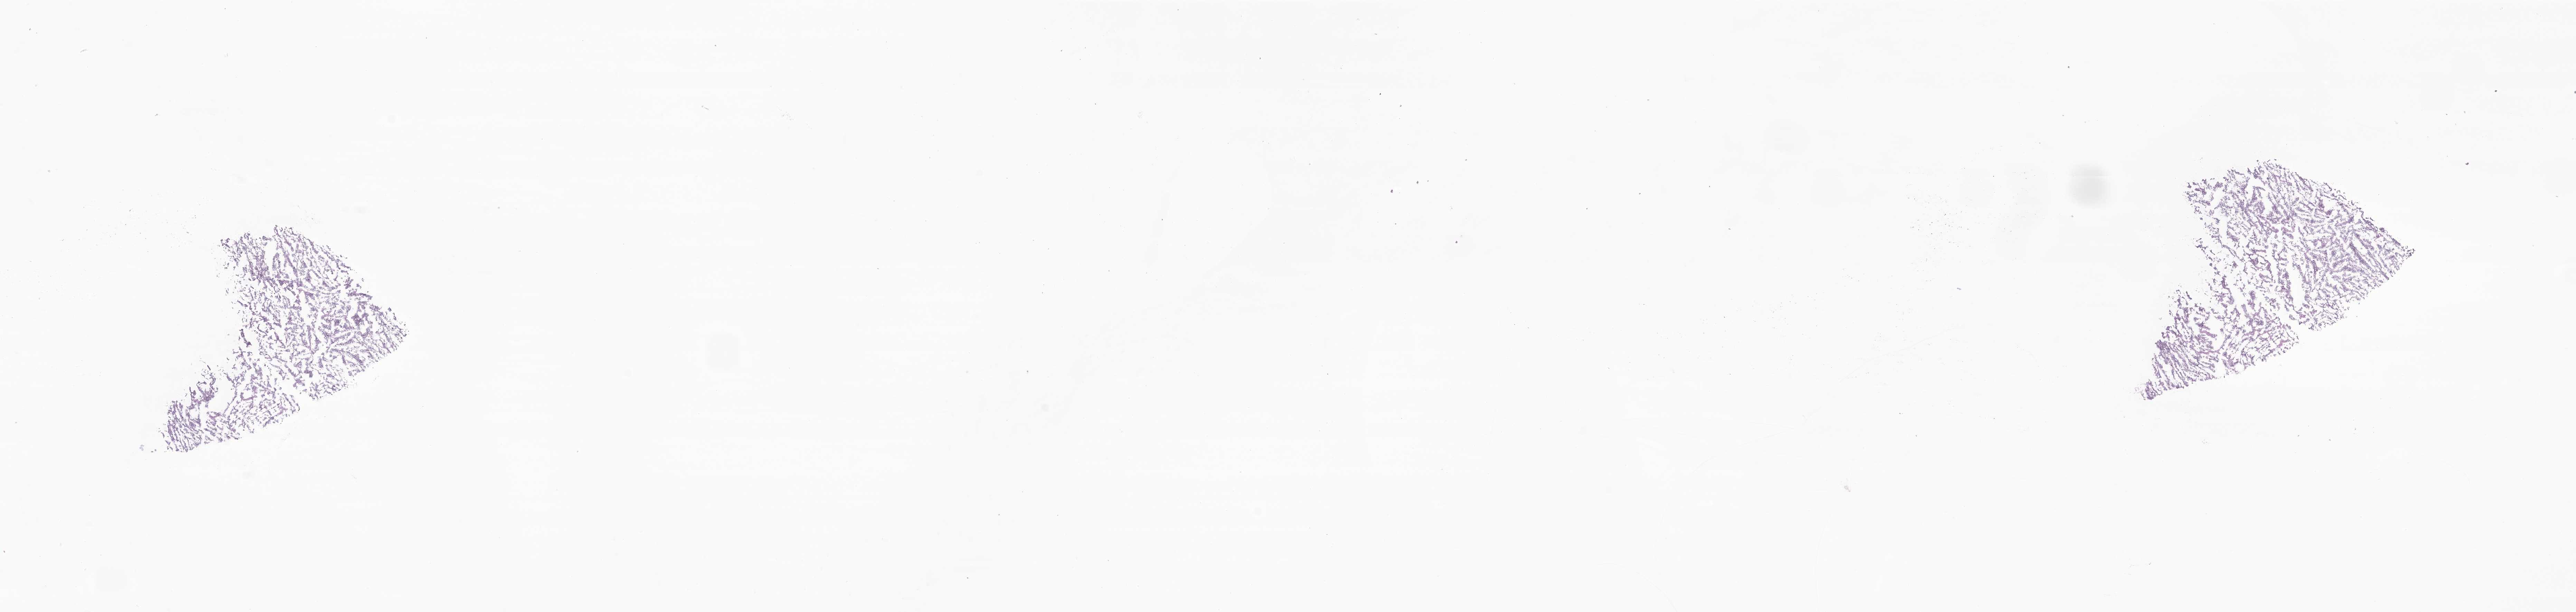
Haematoxylin and eosin whole-slide image of tumor tissue from the frontal lobe — shown as a low-resolution overview of the whole scanned area (about 31.4 x 7.5 mm). Frozen section (OCT-embedded). Patient: female, age 122 months (10 years 2 months).
Recorded diagnosis: Neoplasm, uncertain whether benign or malignant.